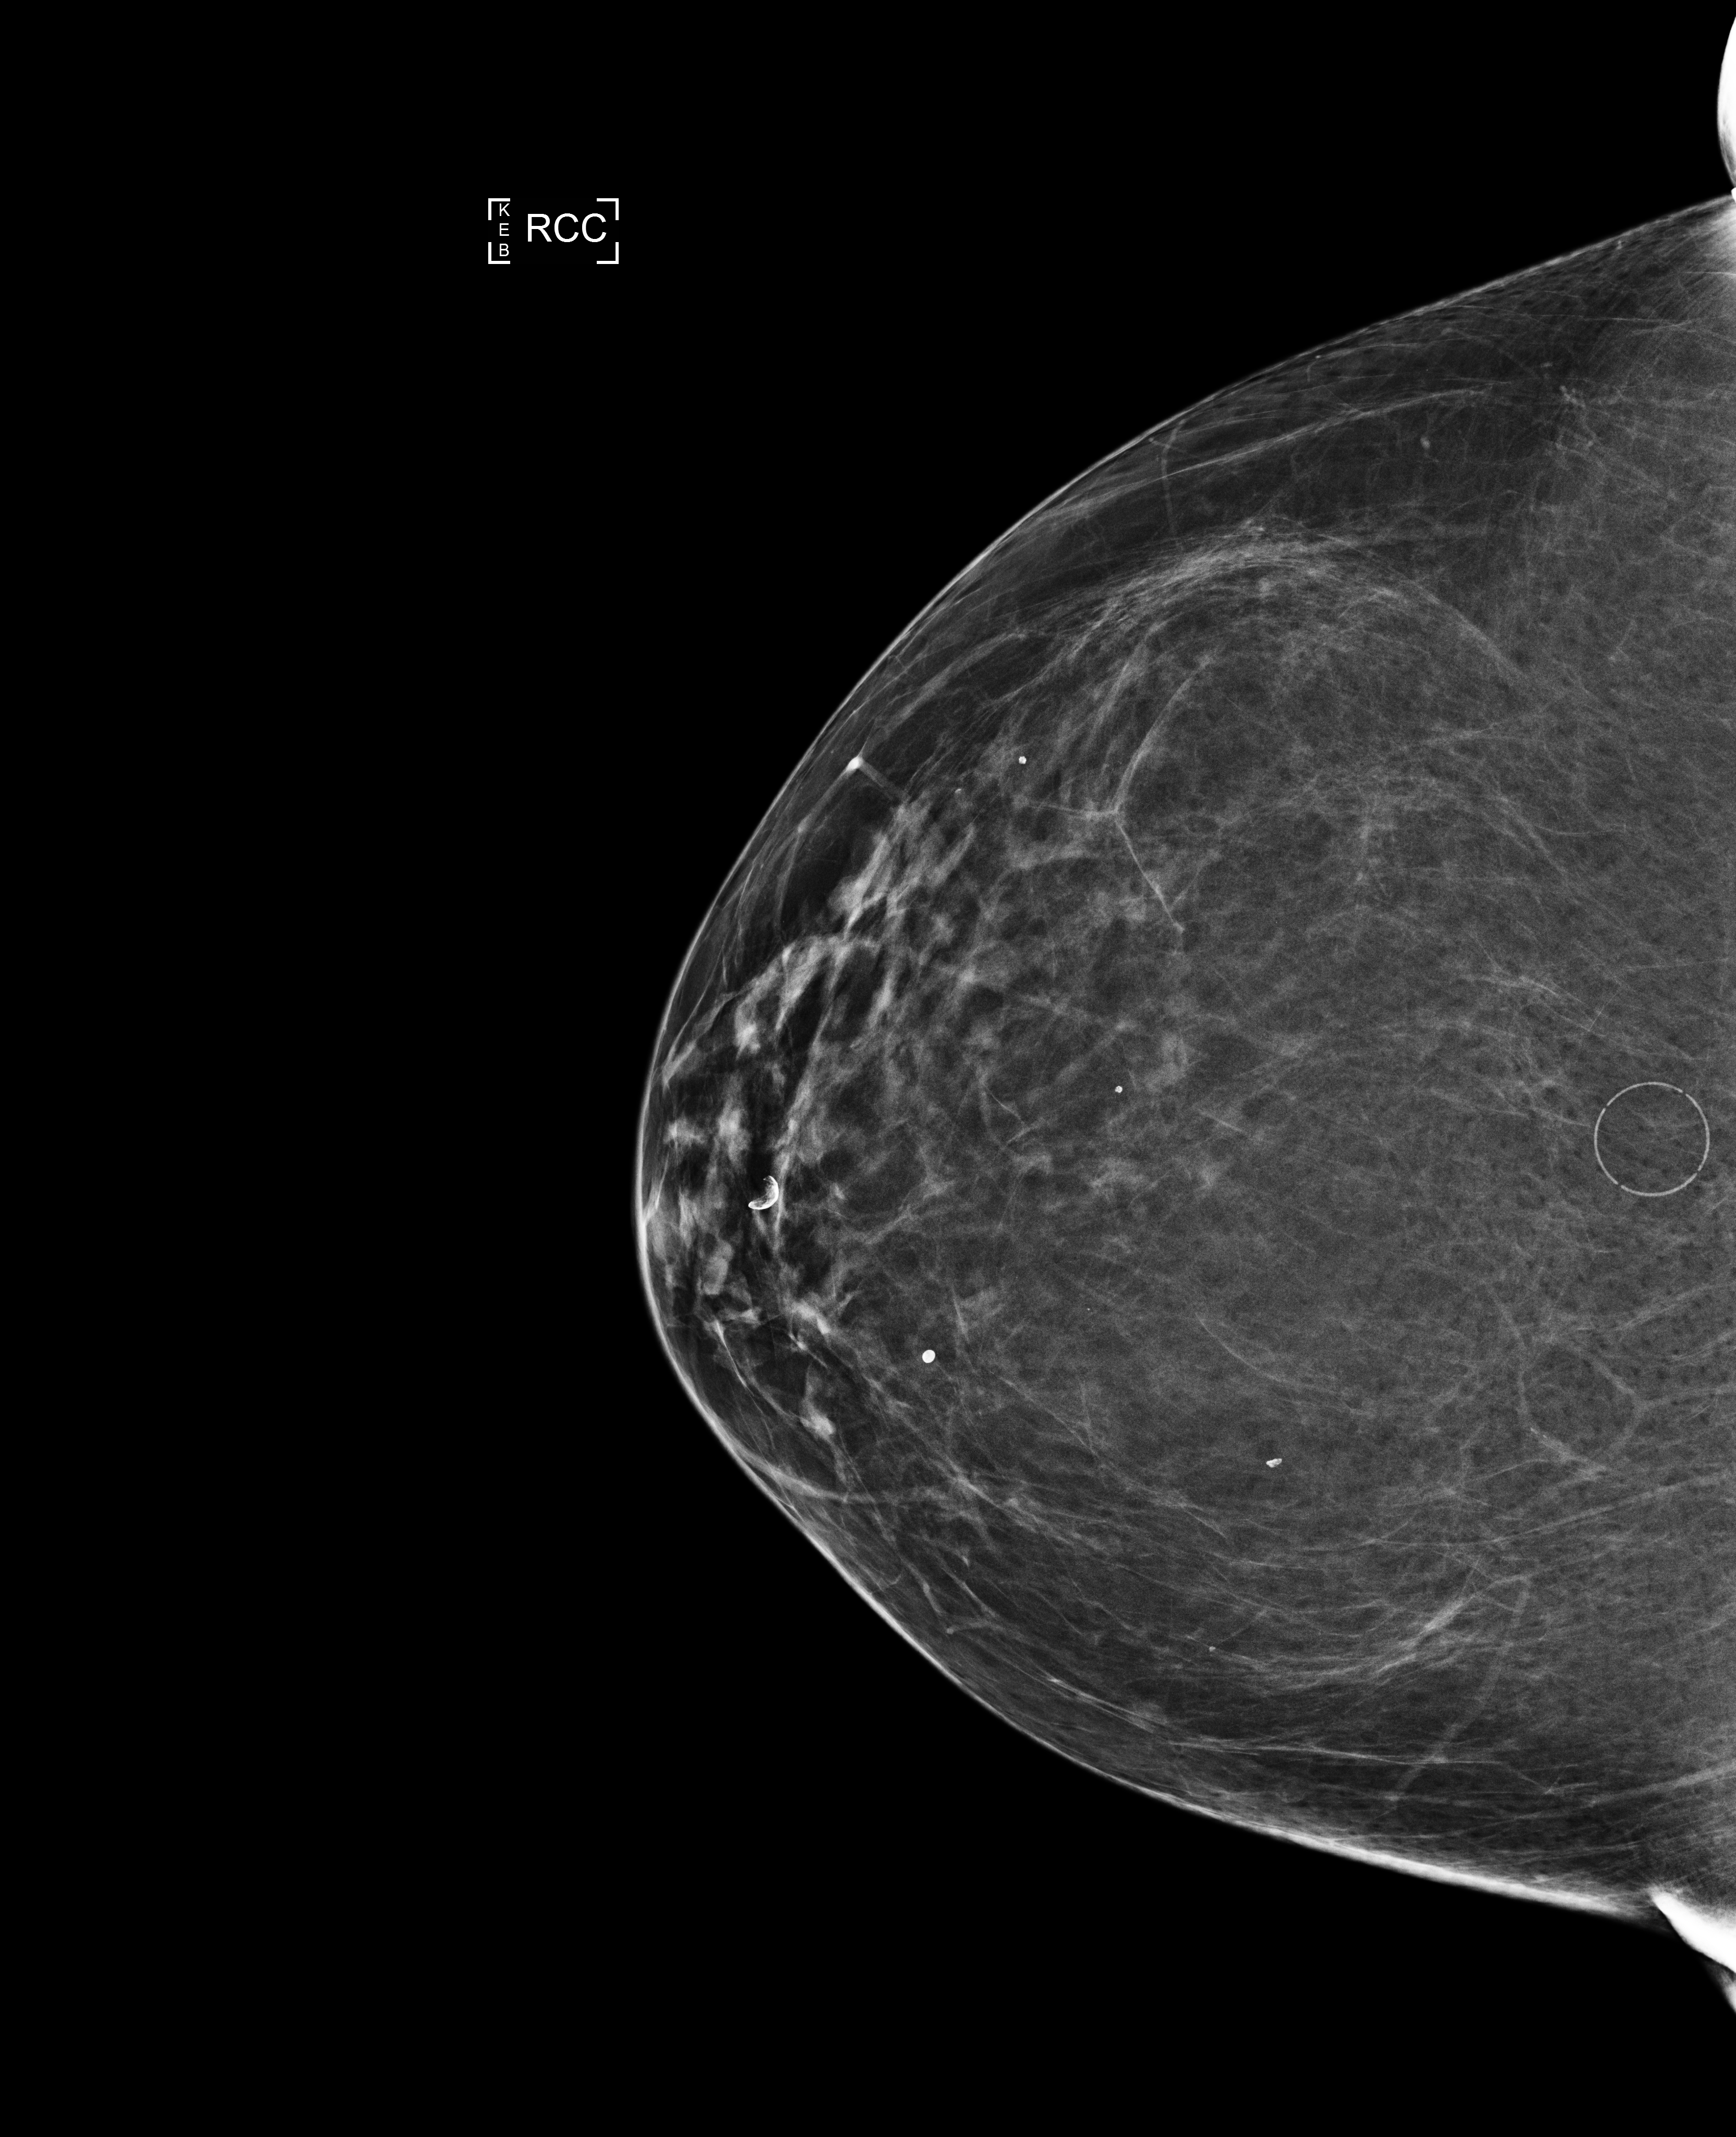
Screening examination, compressed breast thickness 65 mm. Patient aged 67 years (female).
Image type: full-field digital mammogram. Breast: right. Projection: CC view.